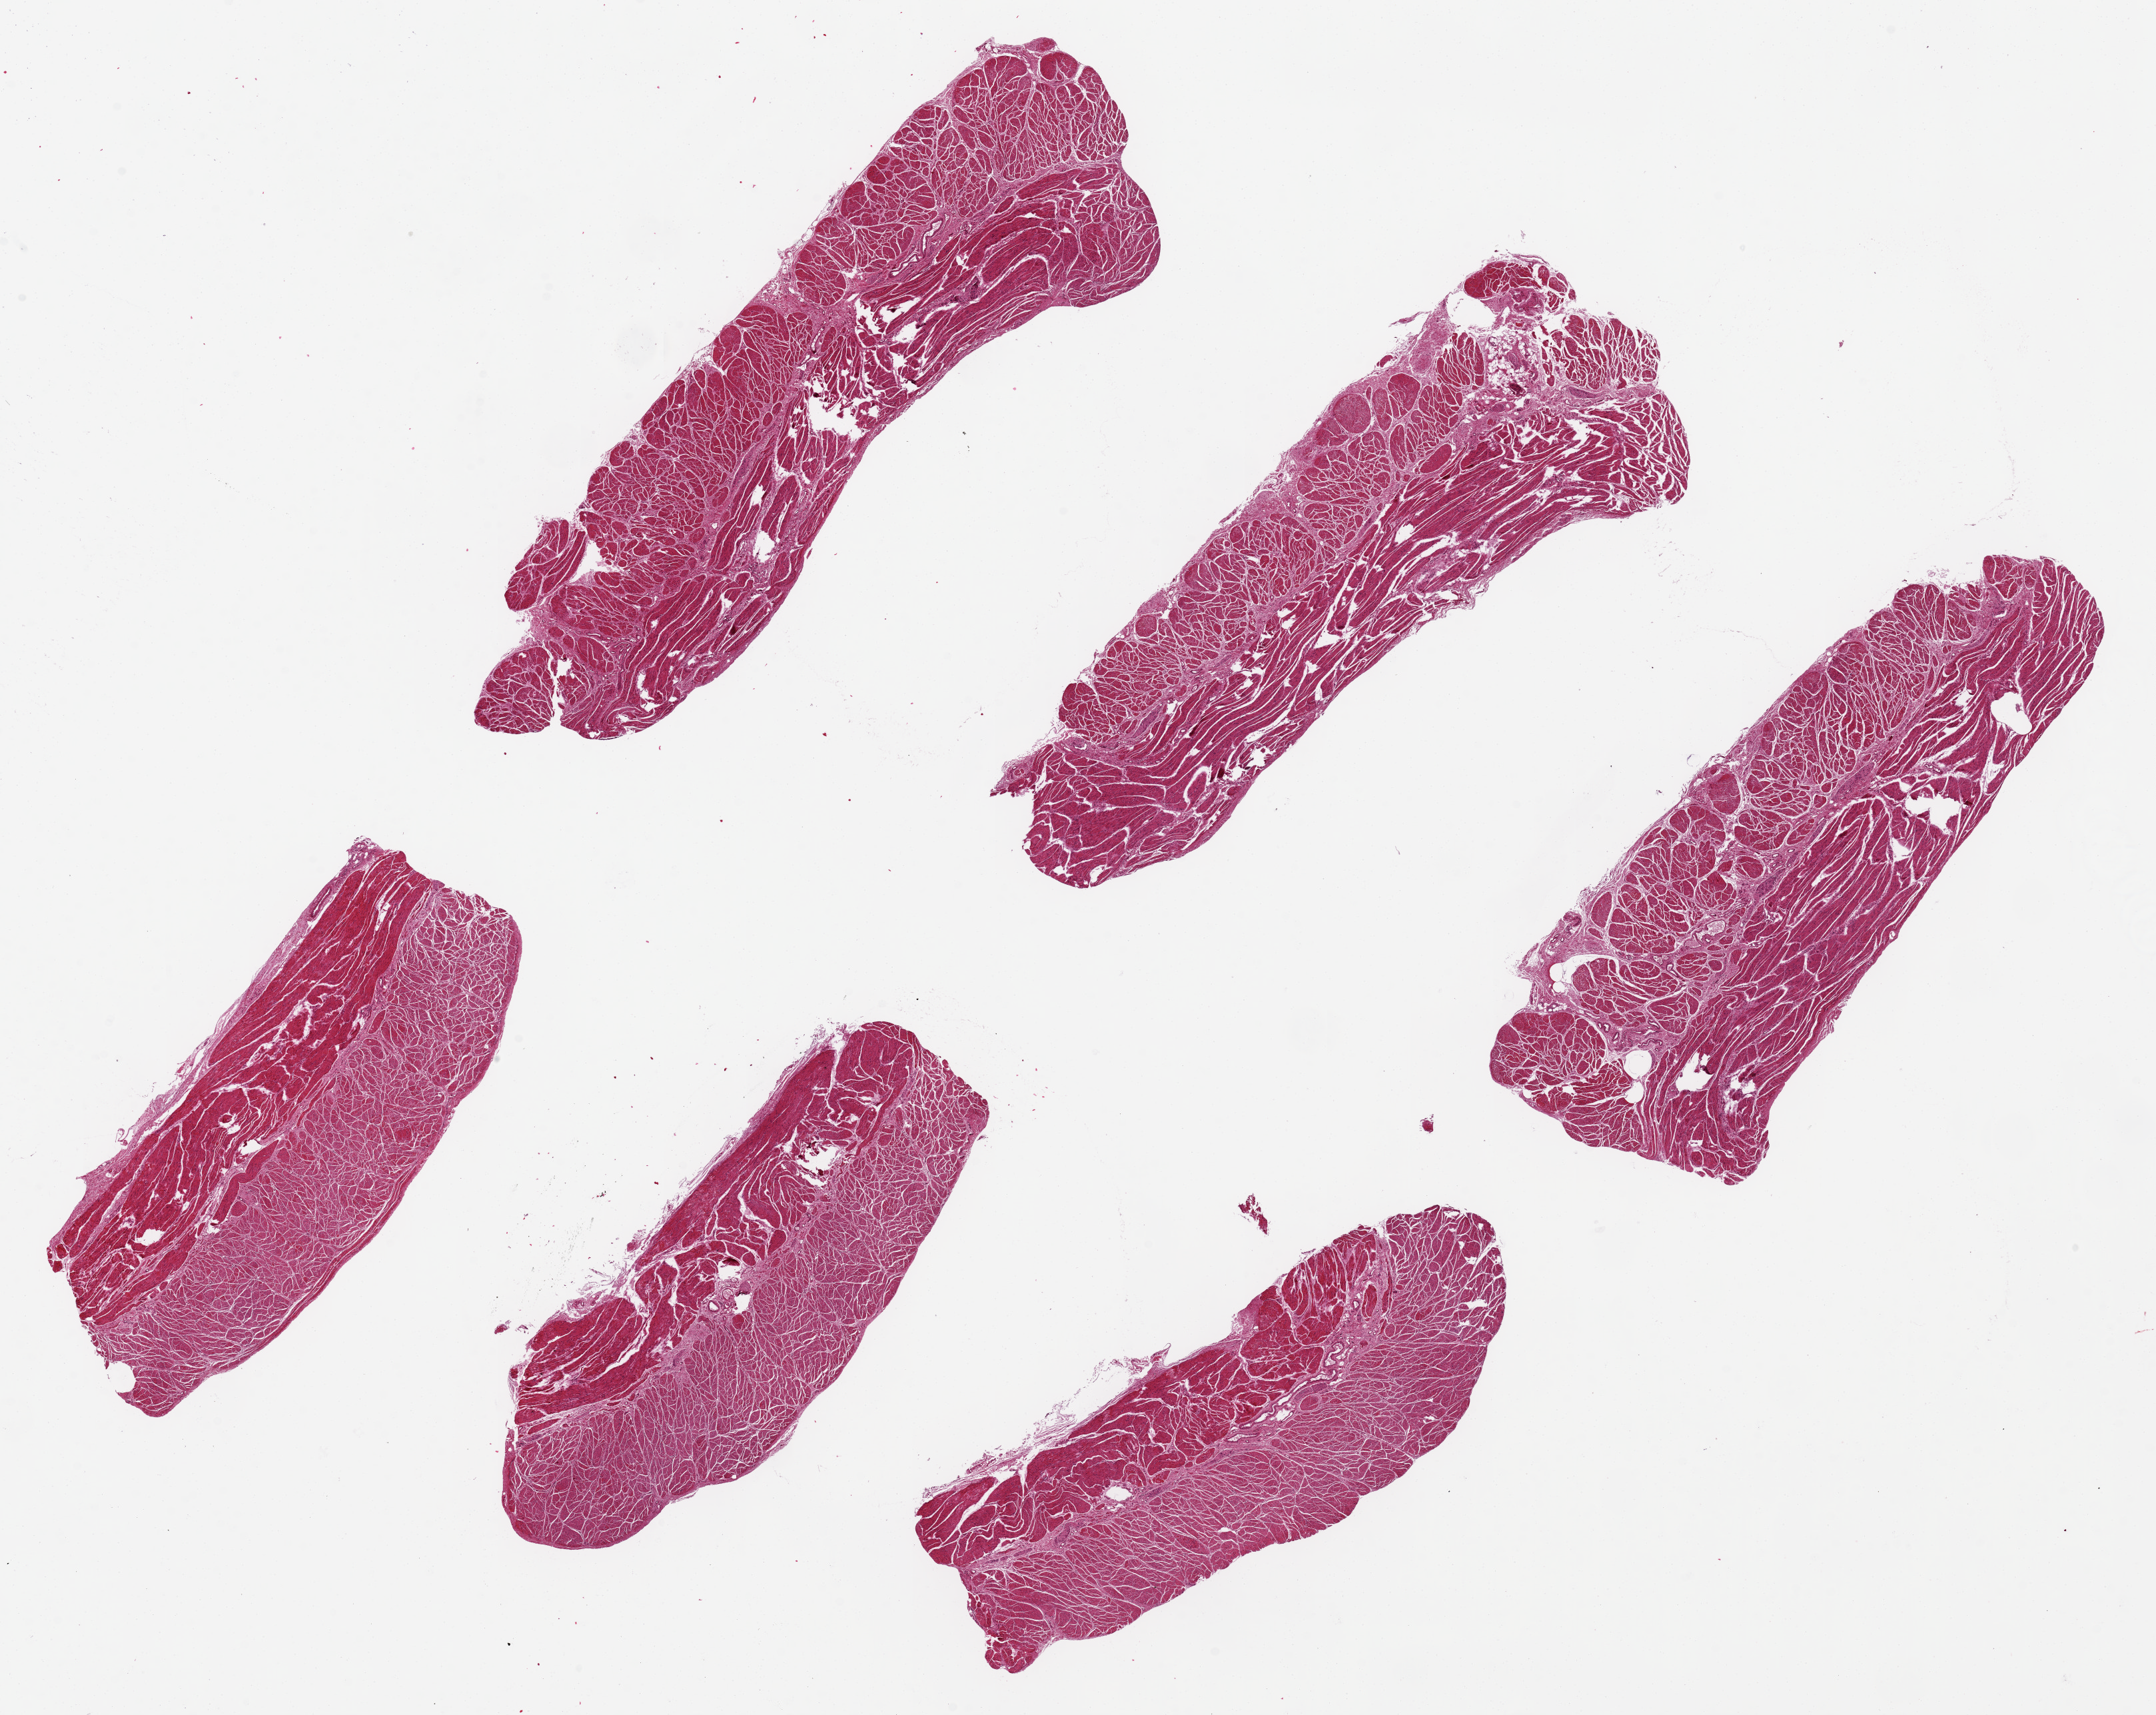
Whole-slide image, haematoxylin and eosin stain — whole scanned area (about 25.6 x 20.4 mm, acquisition: 20x scan) shown as a low-resolution overview. PAXgene-fixed, paraffin-embedded tissue. Target tissue: esophageal muscle. Tissue donor sample. Donor sex: male.
Reviewer comment on this tissue sample: 6 pieces 10.5x3.3 mm; moderate tissue tears.